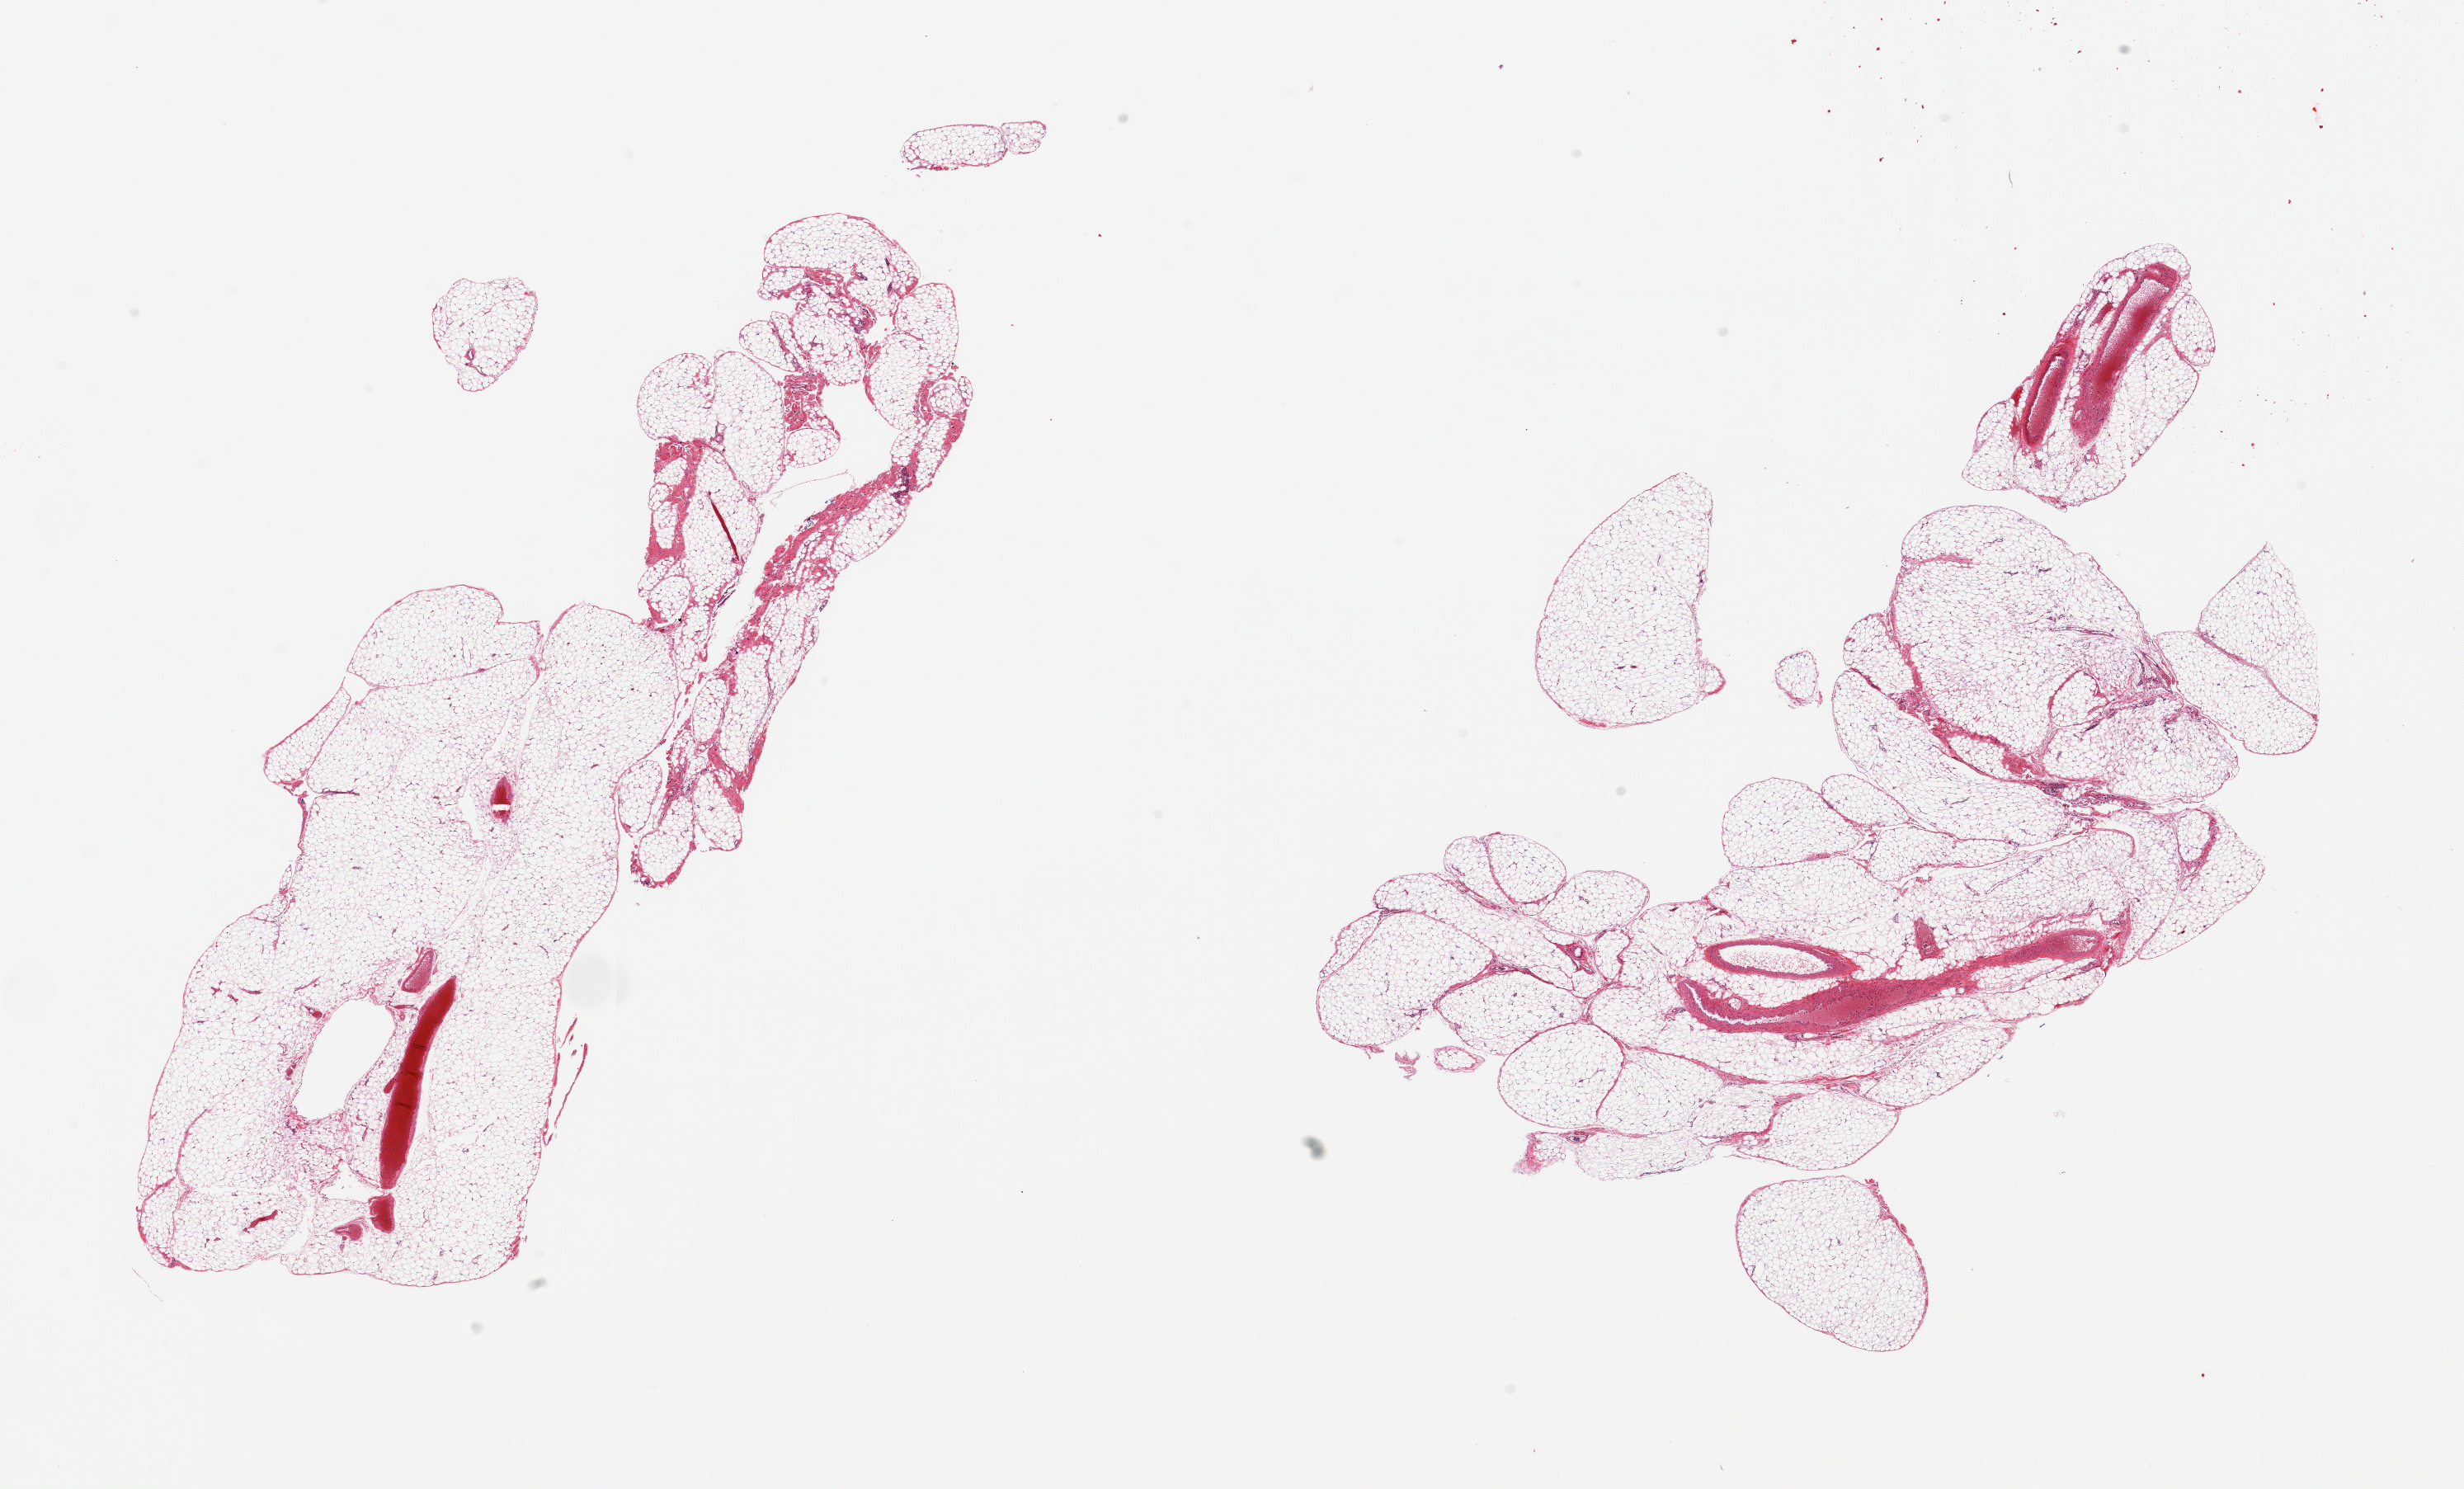
Whole-slide image, haematoxylin and eosin stain, a low-resolution overview of the entire scanned area, about 23.6 x 14.3 mm (acquisition: 20x scan). PAXgene-fixed paraffin-embedded (PFPE) section. Sampled site (target tissue): omentum. Tissue donor sample. Male donor.
Reviewer comment on this tissue sample: 2 pieces; fat with few larger vessels.